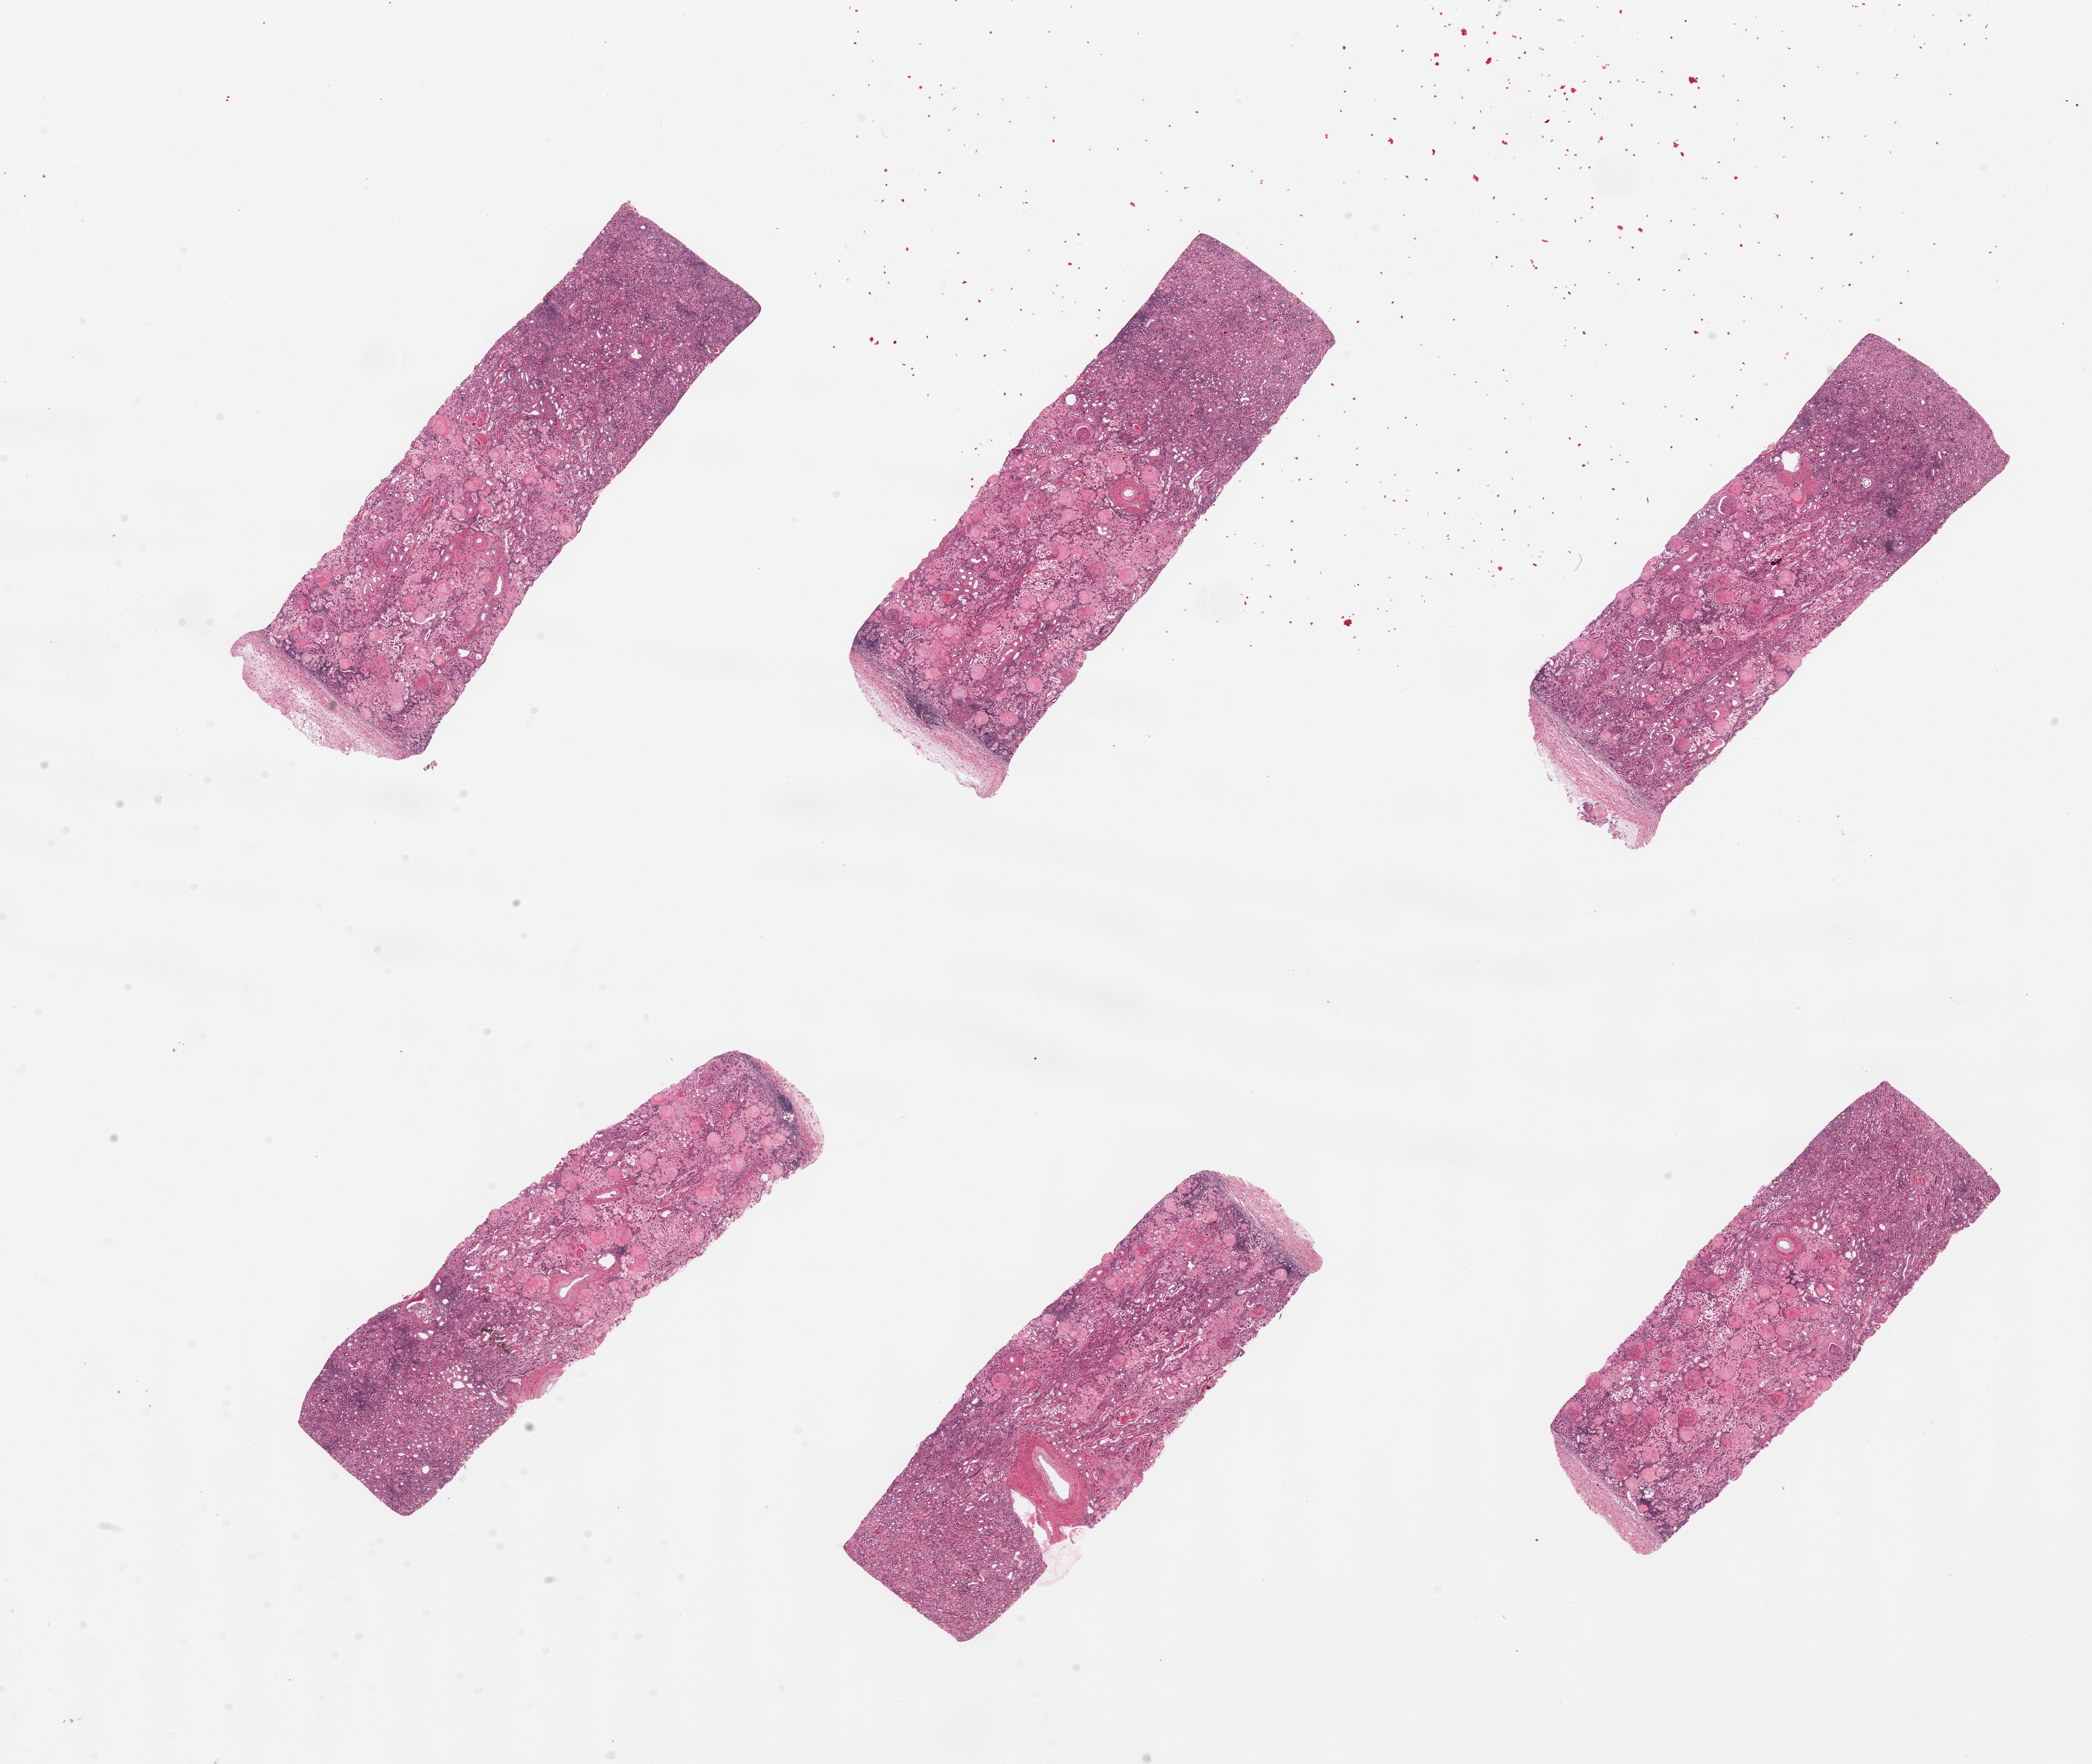
Hematoxylin and eosin (H&E) whole-slide image, whole scanned area (about 25.6 x 21.6 mm) shown as a low-resolution overview; PAXgene-fixed paraffin-embedded (PFPE) section; target tissue: renal cortex; donor tissue sample.
Pathologist's review note for this sample: 6 pieces, glomeruli present. Advanced glomerular sclerosis/chronic nephritis with thyroidization of tubules.